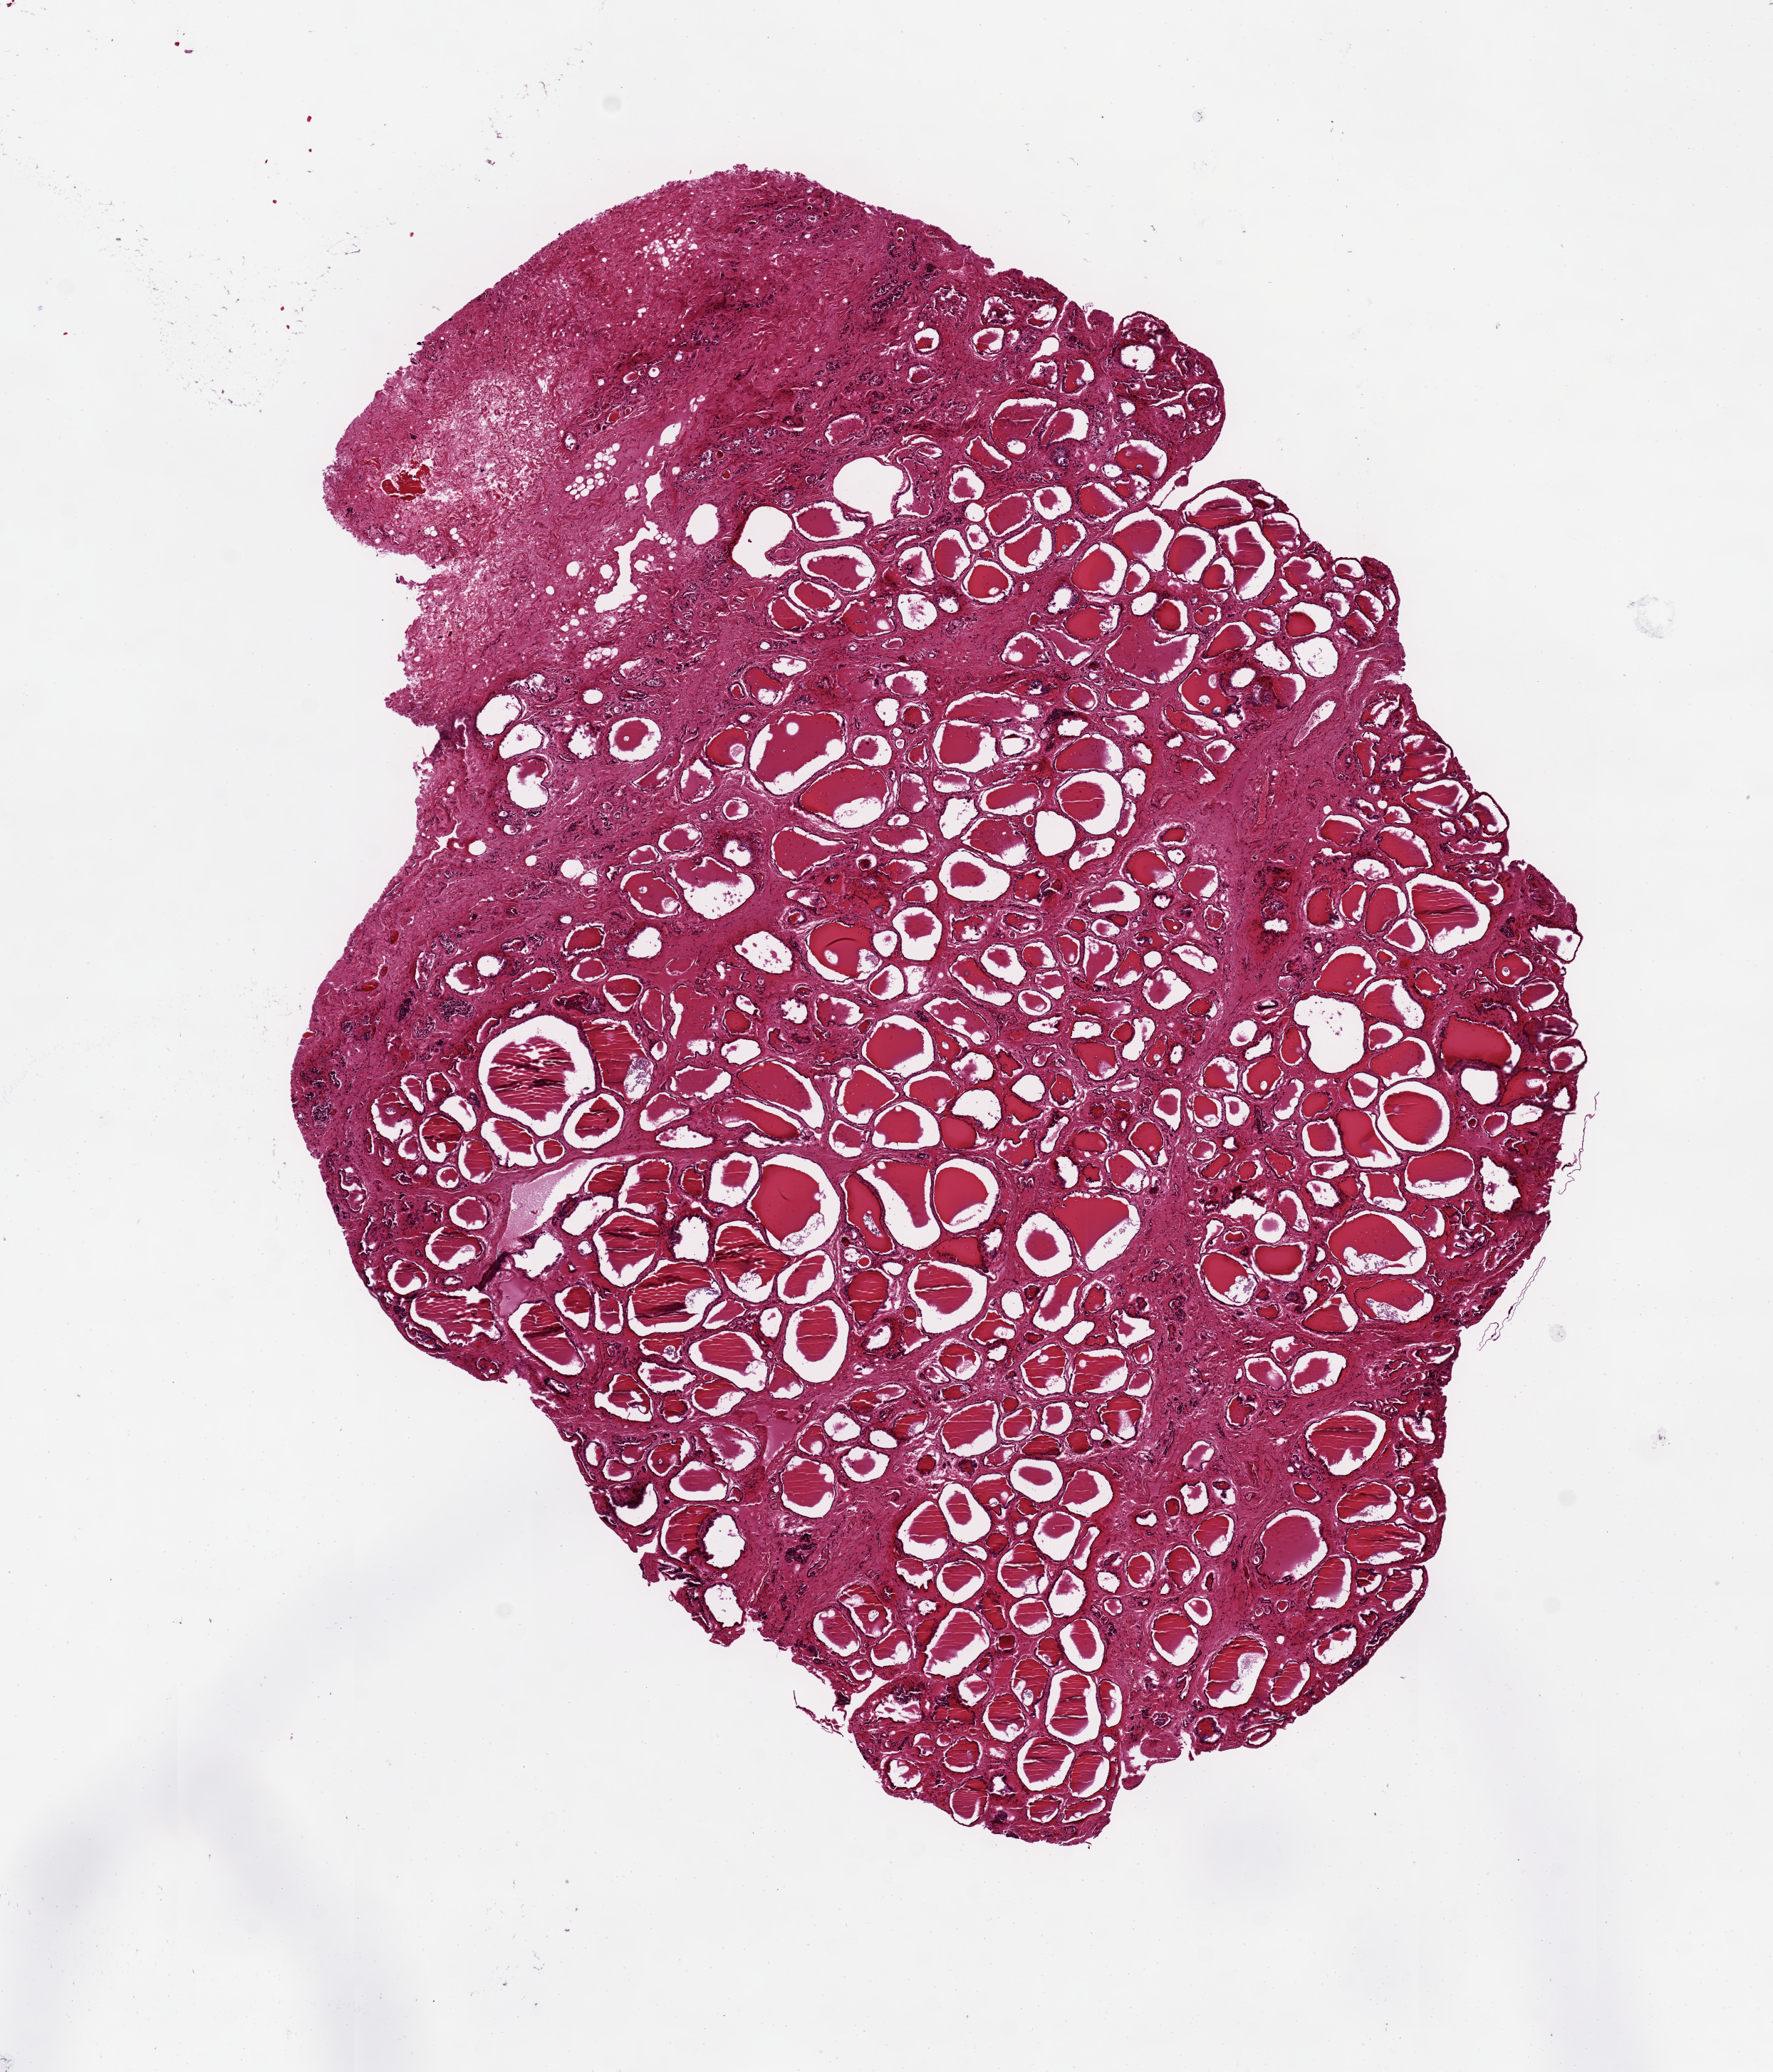
Whole-slide image, hematoxylin and eosin (H&E) stain, shown as a low-resolution overview of the whole scanned area (about 9.8 x 11.5 mm, from a 20x scan), PAXgene-fixed, paraffin-embedded tissue, target tissue: thyroid, donor tissue sample. Male donor.
Pathologist's review note for this sample: Focal fibrosis, 20%. 9x7 mm.